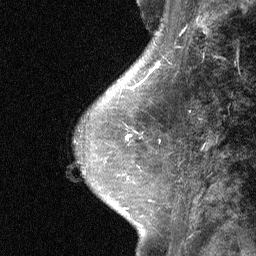
Breast MRI (dynamic contrast-enhanced), one sagittal slice; position 22 of 64 along the scan axis; dynamic contrast-enhanced study with each time point stored as its own series, time point 2 of 3 at this slice position (early post-contrast, ordered by acquisition time); 1.5 T; TE 4.8 ms, TR 27 ms; 2 mm slice thickness; 256 × 256 image matrix, field of view 180 × 180 mm. Patient: female, 42 years. From the clinical record (not read from this slice): setting: breast cancer imaged before/during neoadjuvant chemotherapy; receptor status: triple-negative.
Annotated regions visible in this slice (semi-automatic segmentation, software-assisted and operator-edited):
- analysis volume of interest (the breast-tissue region the enhancement analysis was run in; not a lesion): bounding box (x1, y1, x2, y2) in pixels: (99, 117, 174, 187)
- tumour enhancement mask (voxels above the 90 % enhancement threshold inside the analysis volume of interest): (126, 135, 131, 140)